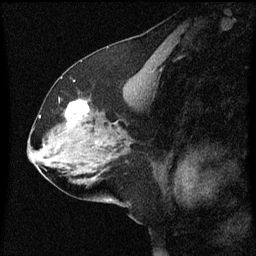
Breast MRI (dynamic contrast-enhanced), one sagittal slice. Slice 31 of 60 in the series (ordered by position). Dynamic contrast-enhanced series, image 2 of 3 at this slice position (ordered by acquisition). 1.5 T. TE 4.2 ms, TR 8 ms. 2 mm slice thickness. 256 × 256 image matrix. Female patient, age 58 years.
Structures marked on this image (semi-automatic segmentation, software-assisted and operator-edited):
- analysis volume of interest (the breast-tissue region the enhancement analysis was run in; not a lesion): bounding box (x1, y1, x2, y2) in pixels: (56, 100, 95, 137)
- tumour enhancement mask (voxels above the 70 % enhancement threshold inside the analysis volume of interest): (66, 100, 89, 123)